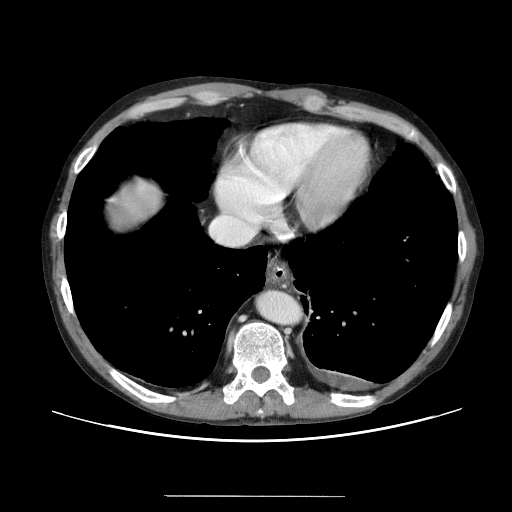
Contrast-enhanced abdominal CT (liver protocol), one axial slice; reconstruction kernel STANDARD; 120 kVp; soft-tissue window (W 400 / L 40 HU); 512 × 512 image matrix. Case-level facts recorded for this patient, not image findings: diagnosis: hepatocellular carcinoma (patient treated with transarterial chemoembolisation; whether this scan precedes or follows treatment is not stated here); TNM stage (as recorded): Stage-IVB; Child-Pugh class: B; tumour differentiation: poorly differentiated; tumour nodularity: multinodular.
Structures marked on this image (semi-automatically segmented with operator editing):
- liver parenchyma outside the tumour (the mass and vessels are separate outlines, so this box may not span the whole liver): box from (x=94, y=174) to (x=168, y=244) px